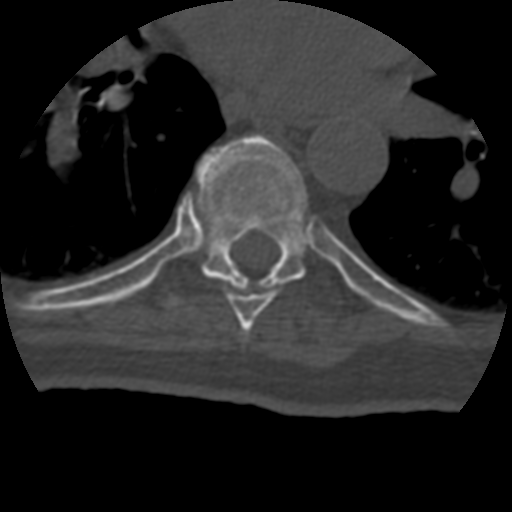
CT including the spine, one axial slice. Slice 270 of 399 in the series (ordered by position). Reconstruction kernel STANDARD. 120 kVp. Bone window (W 1800 / L 400 HU). 1.25 mm slice thickness. 512 × 512 image matrix. Patient age 69 years. From the clinical record (not read from this slice): primary cancer: prostate.
Structures marked on this image (semi-automatic segmentation, software-assisted and operator-edited):
- T7 vertebra: box from (x=221, y=281) to (x=276, y=332) px
- T8 vertebra: (x=159, y=135)–(x=336, y=314)